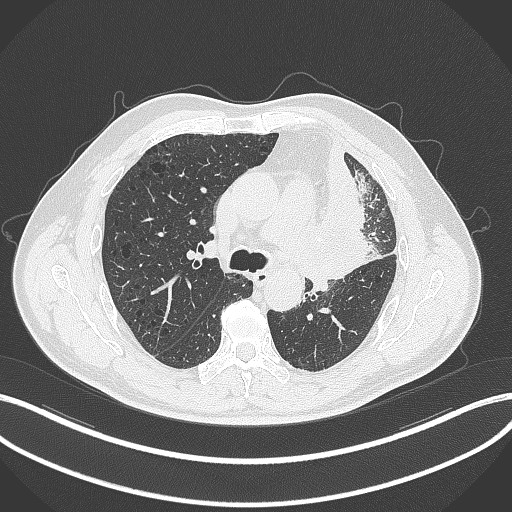
Chest CT, one axial slice; slice 195 of 297 in the series (ordered by position); reconstruction kernel B70f; 120 kVp; lung window (W 1500 / L -600 HU); 1 mm slice thickness; 512 × 512 image matrix. Patient: male, 68 years. Case-level facts recorded for this patient, not image findings: clinical TNM (as recorded): T3 N3 M1.
Annotated regions visible in this slice (bounding box drawn by a radiologist):
- lung tumour (recorded histology: adenocarcinoma): box from (x=318, y=150) to (x=380, y=289) px